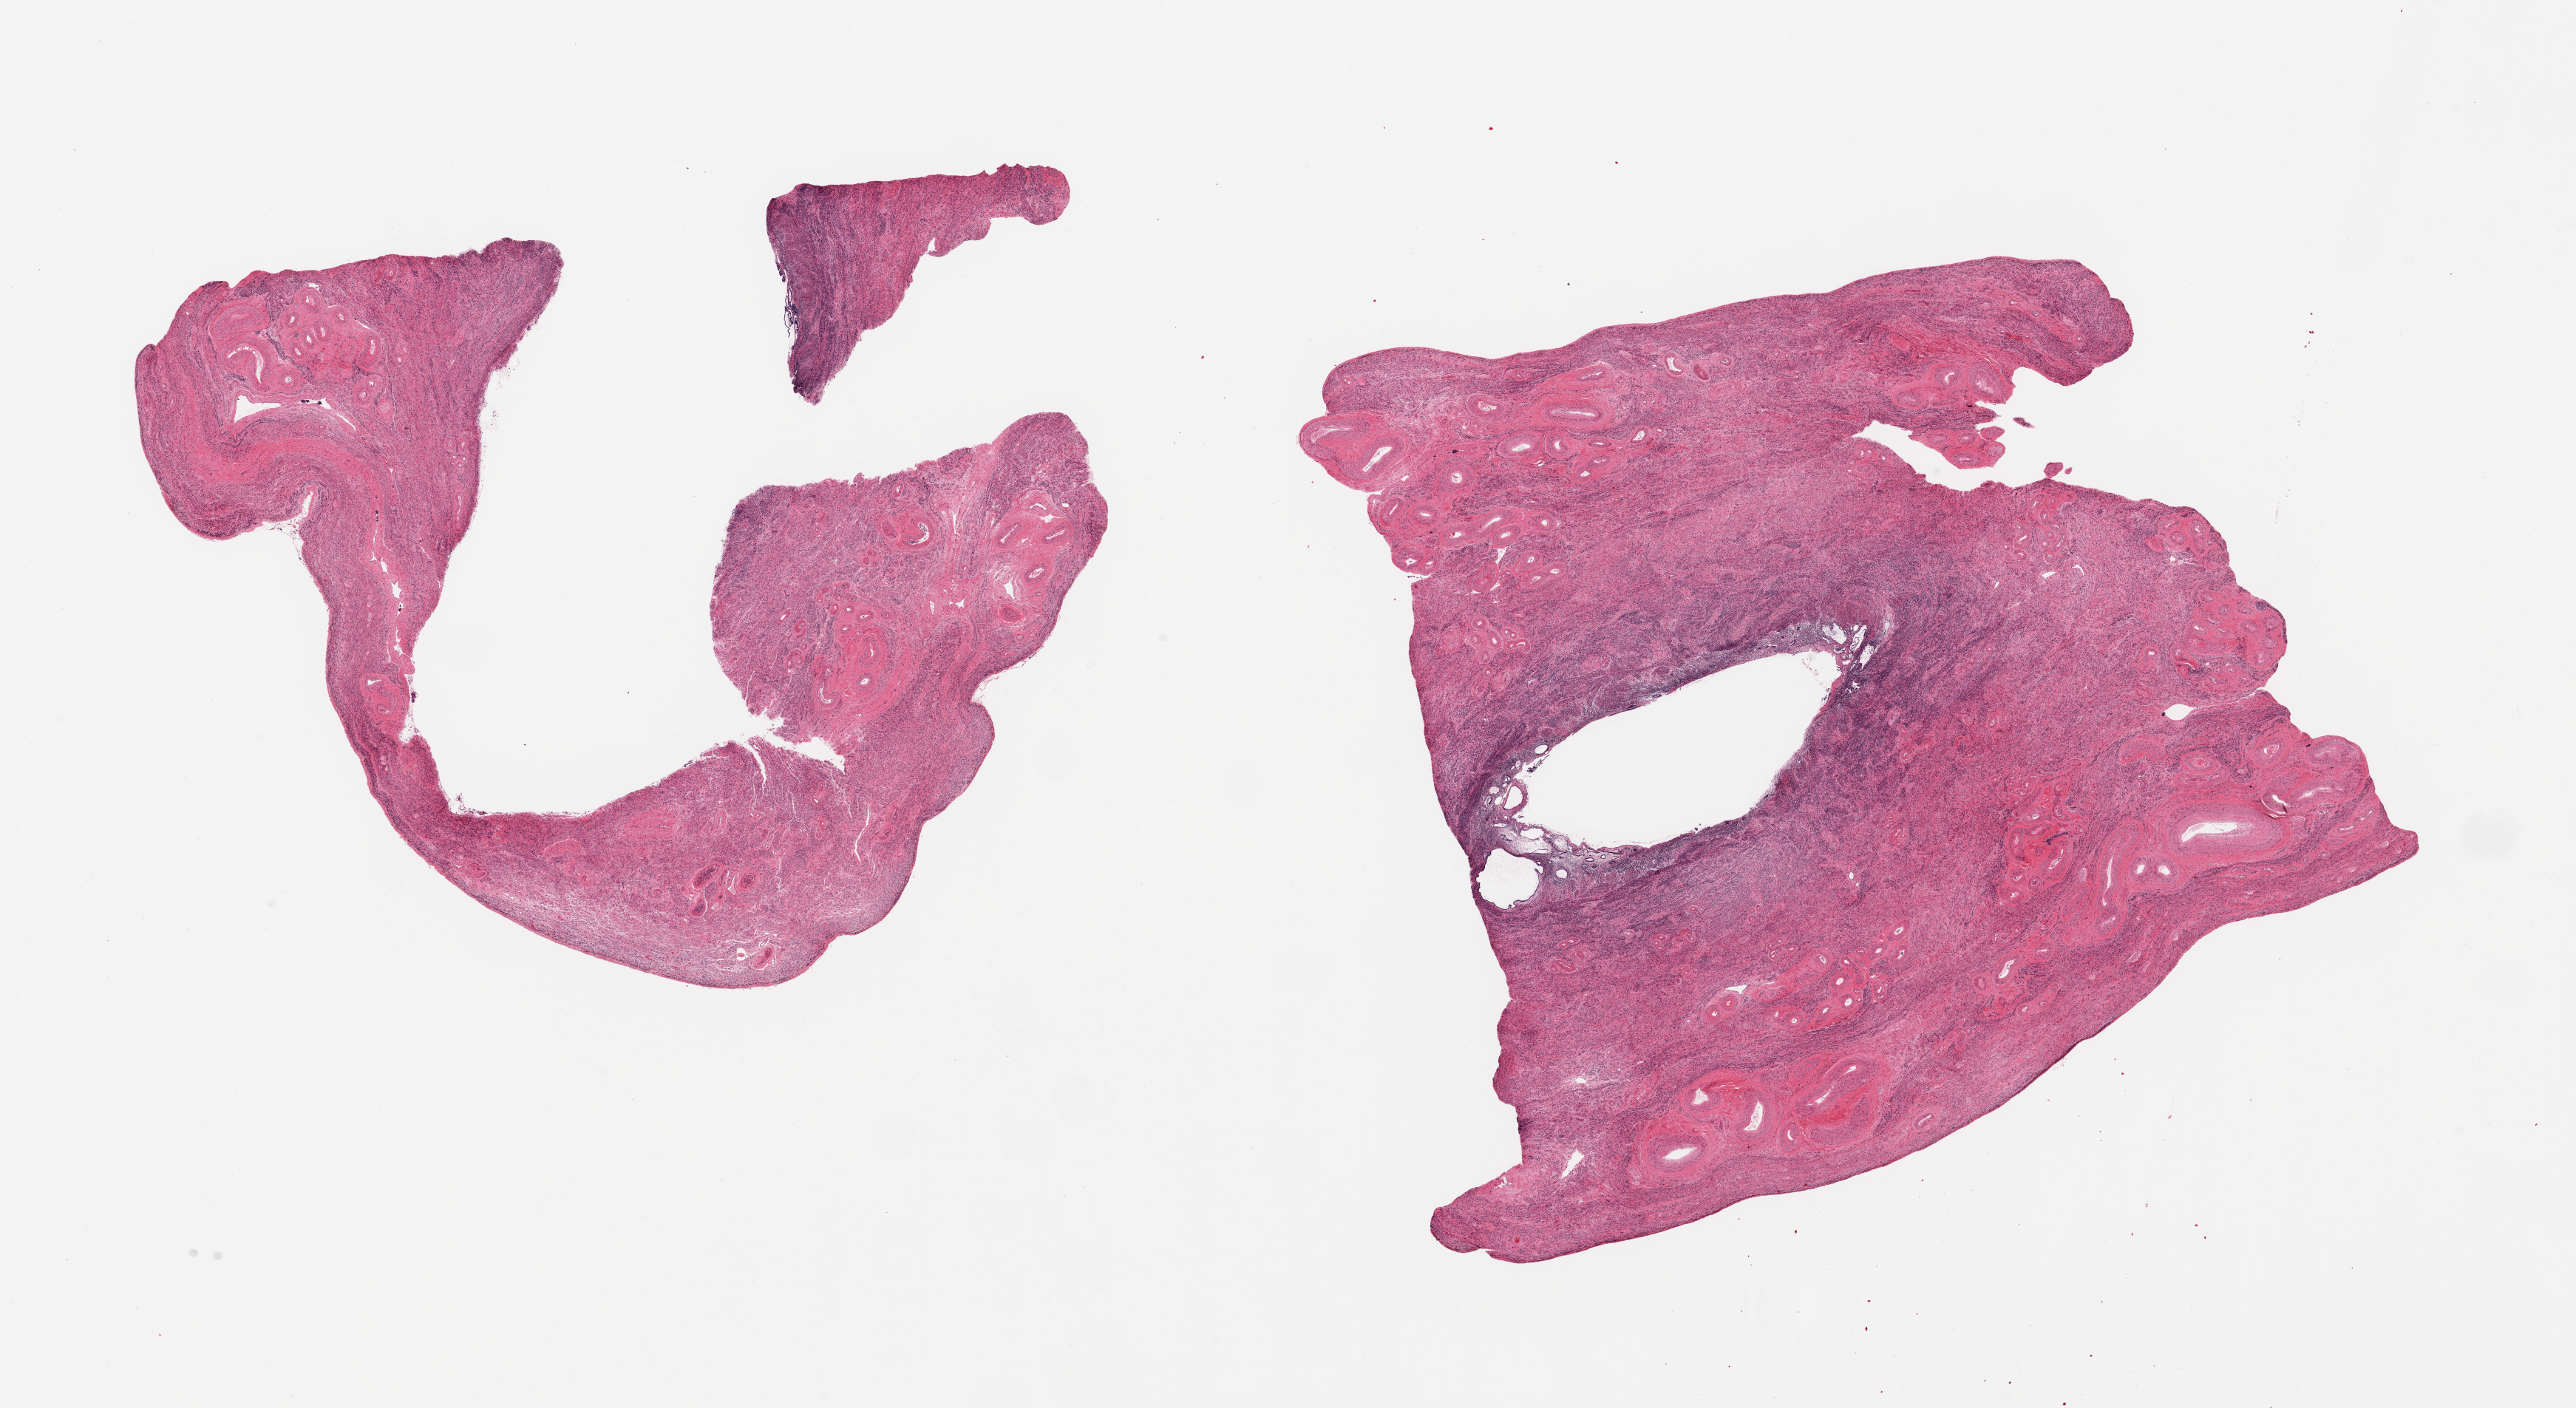
Digitized haematoxylin and eosin-stained section, whole scanned area (about 27.6 x 15.1 mm, from a 20x scan) shown as a low-resolution overview. PAXgene-fixed, paraffin-embedded tissue. Section of uterus (target tissue). Tissue donor sample. Donor sex: female.
Pathologist's review note for this sample: 2 pieces; mostly myometrium, but small component of endometrium with cystic atrophy.